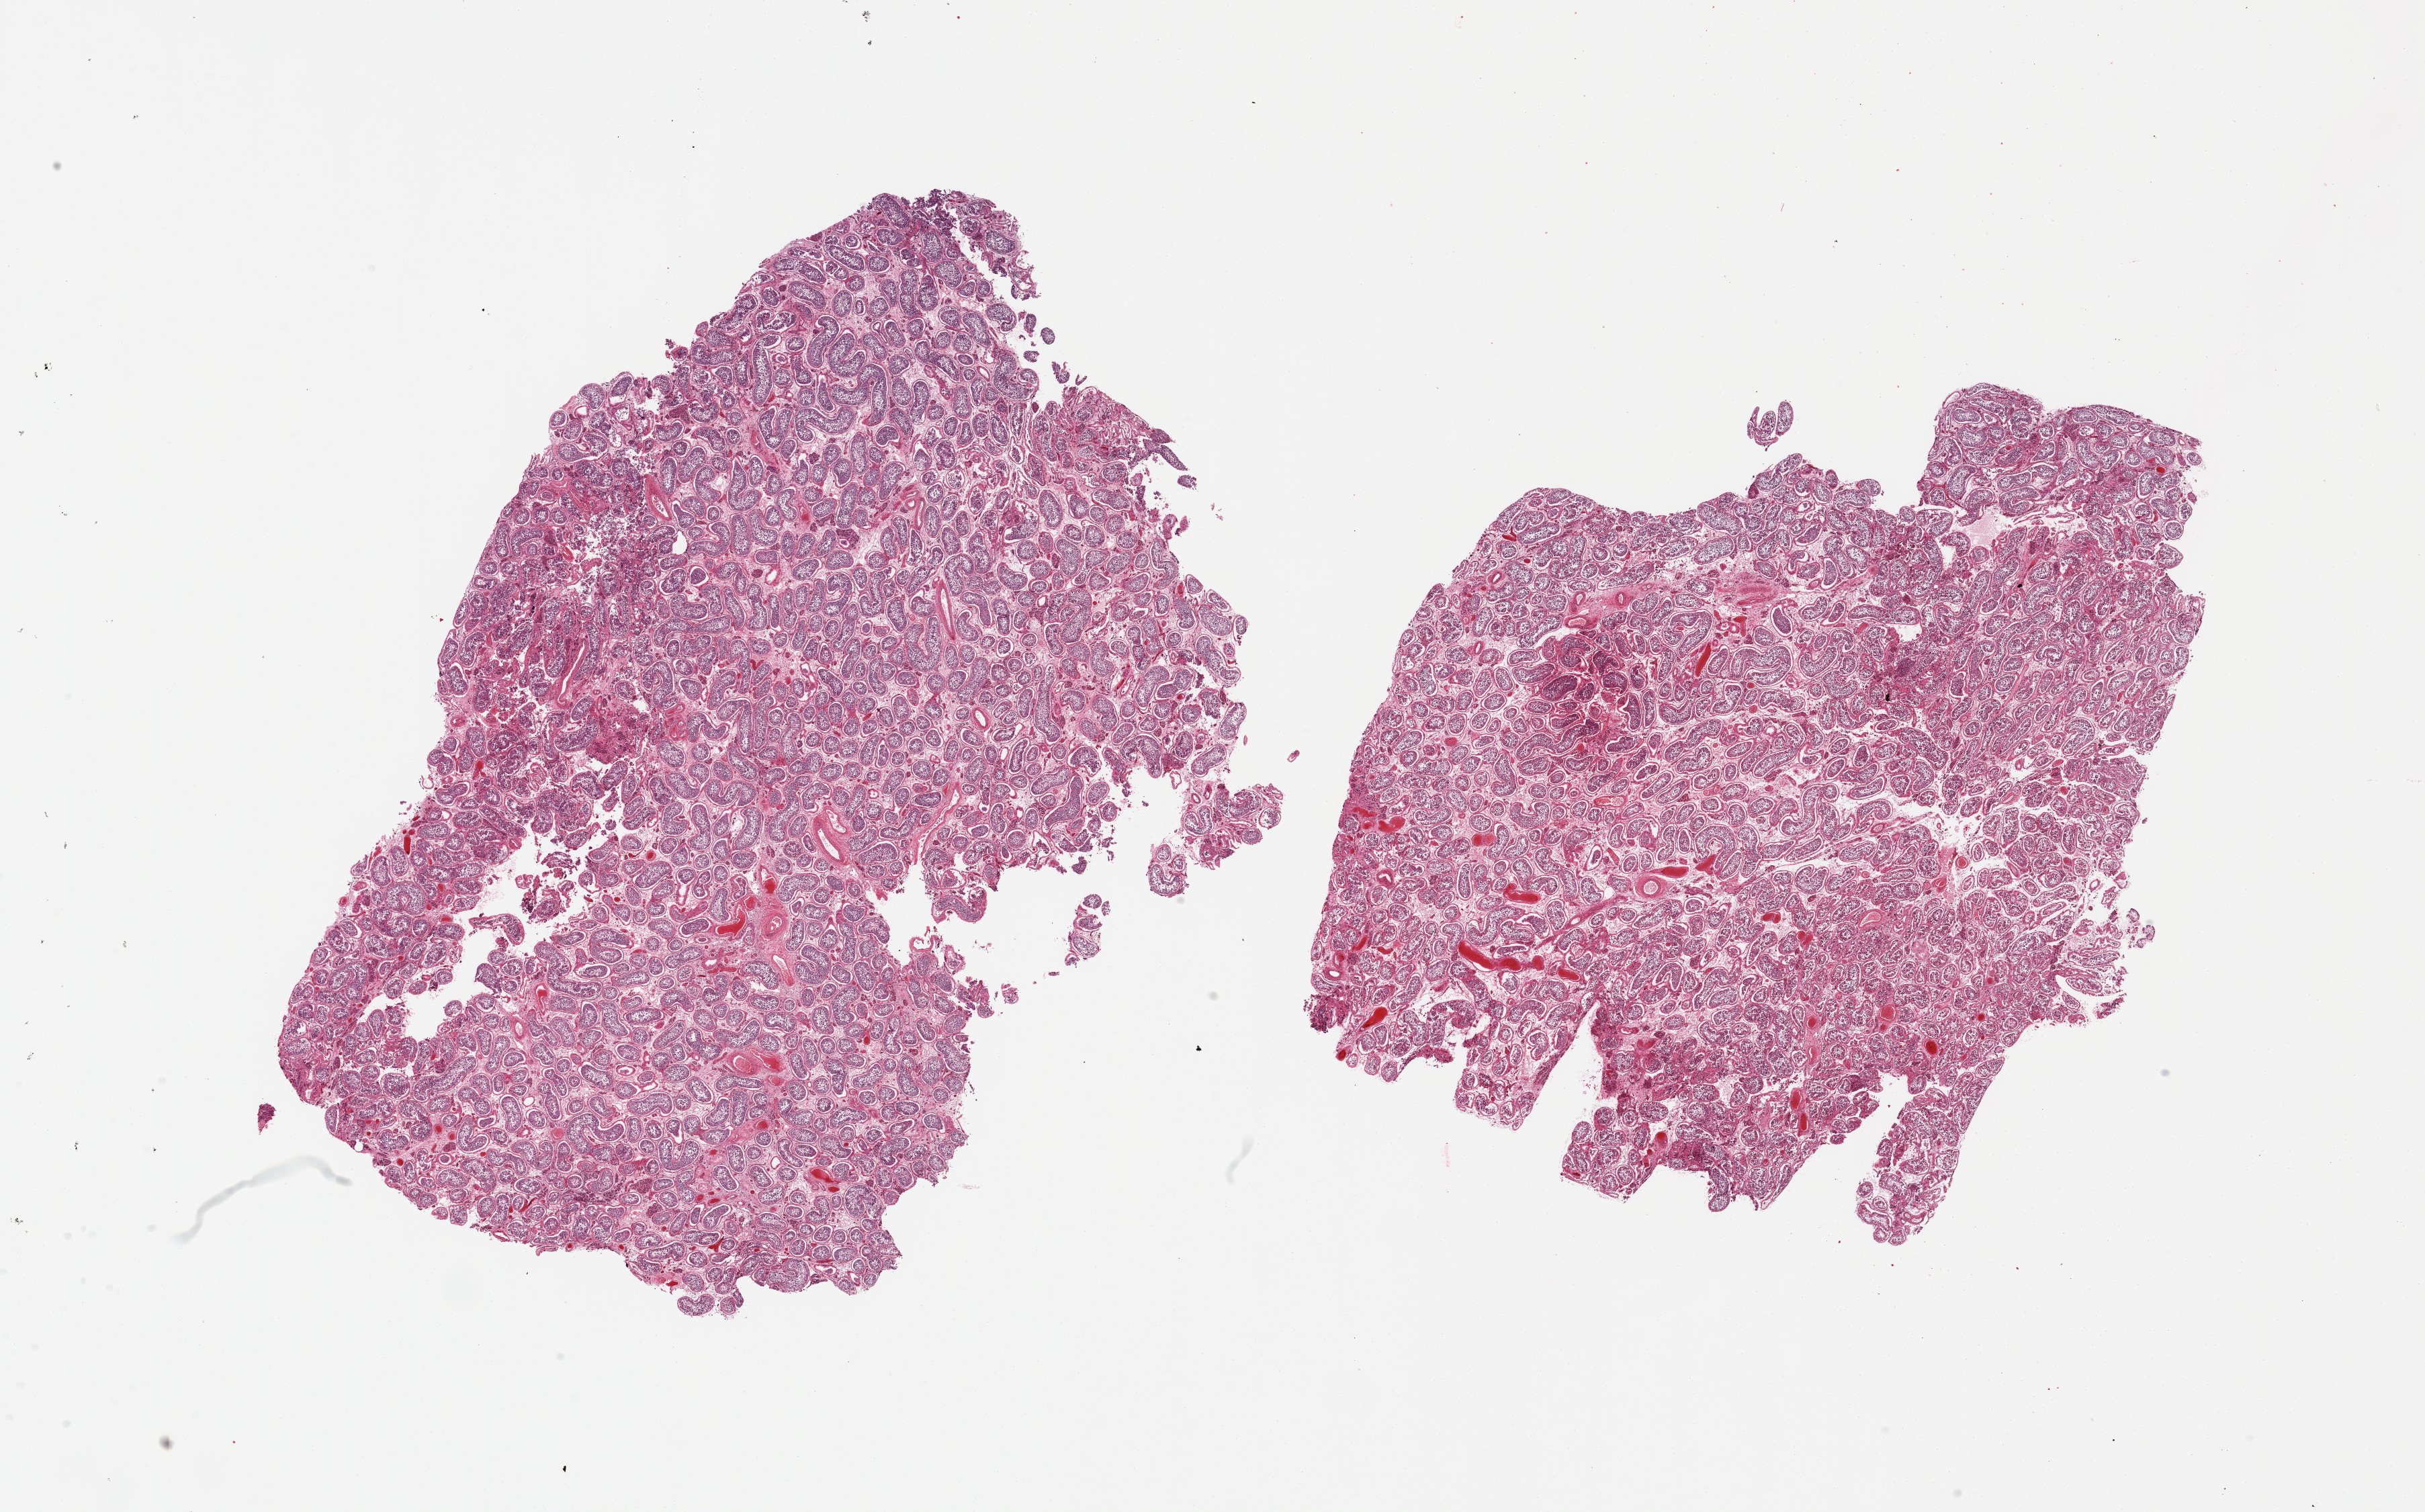
Hematoxylin and eosin (H&E) whole-slide image — a low-resolution overview of the entire scanned area, about 28.5 x 17.8 mm (slide scanned at 20x). PAXgene-fixed paraffin-embedded (PFPE) section. Section of testis (target tissue). Tissue donor sample. Male donor.
• review note (as recorded): 2 pieces; spermatogenesis present